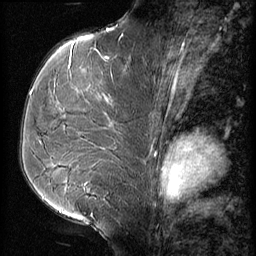
Breast MRI (dynamic contrast-enhanced), one sagittal slice. Slice 34 of 56 in the series (ordered by position). 3 images stored at this slice position (order not interpretable as contrast timing). 1.5 T. TE 4.2 ms, TR 9 ms. 256 × 256 image matrix, field of view 180 × 180 mm. Female patient, age 51 years. Case-level facts recorded for this patient, not image findings: setting: breast cancer imaged before/during neoadjuvant chemotherapy; receptor status: HR-positive, HER2-negative.
Annotated regions visible in this slice (semi-automatic segmentation, software-assisted and operator-edited):
- analysis volume of interest (the breast-tissue region the enhancement analysis was run in; not a lesion): box from (x=23, y=56) to (x=149, y=165) px
- tumour enhancement mask (voxels above the 140 % enhancement threshold inside the analysis volume of interest): (x=75, y=56)–(x=112, y=103)